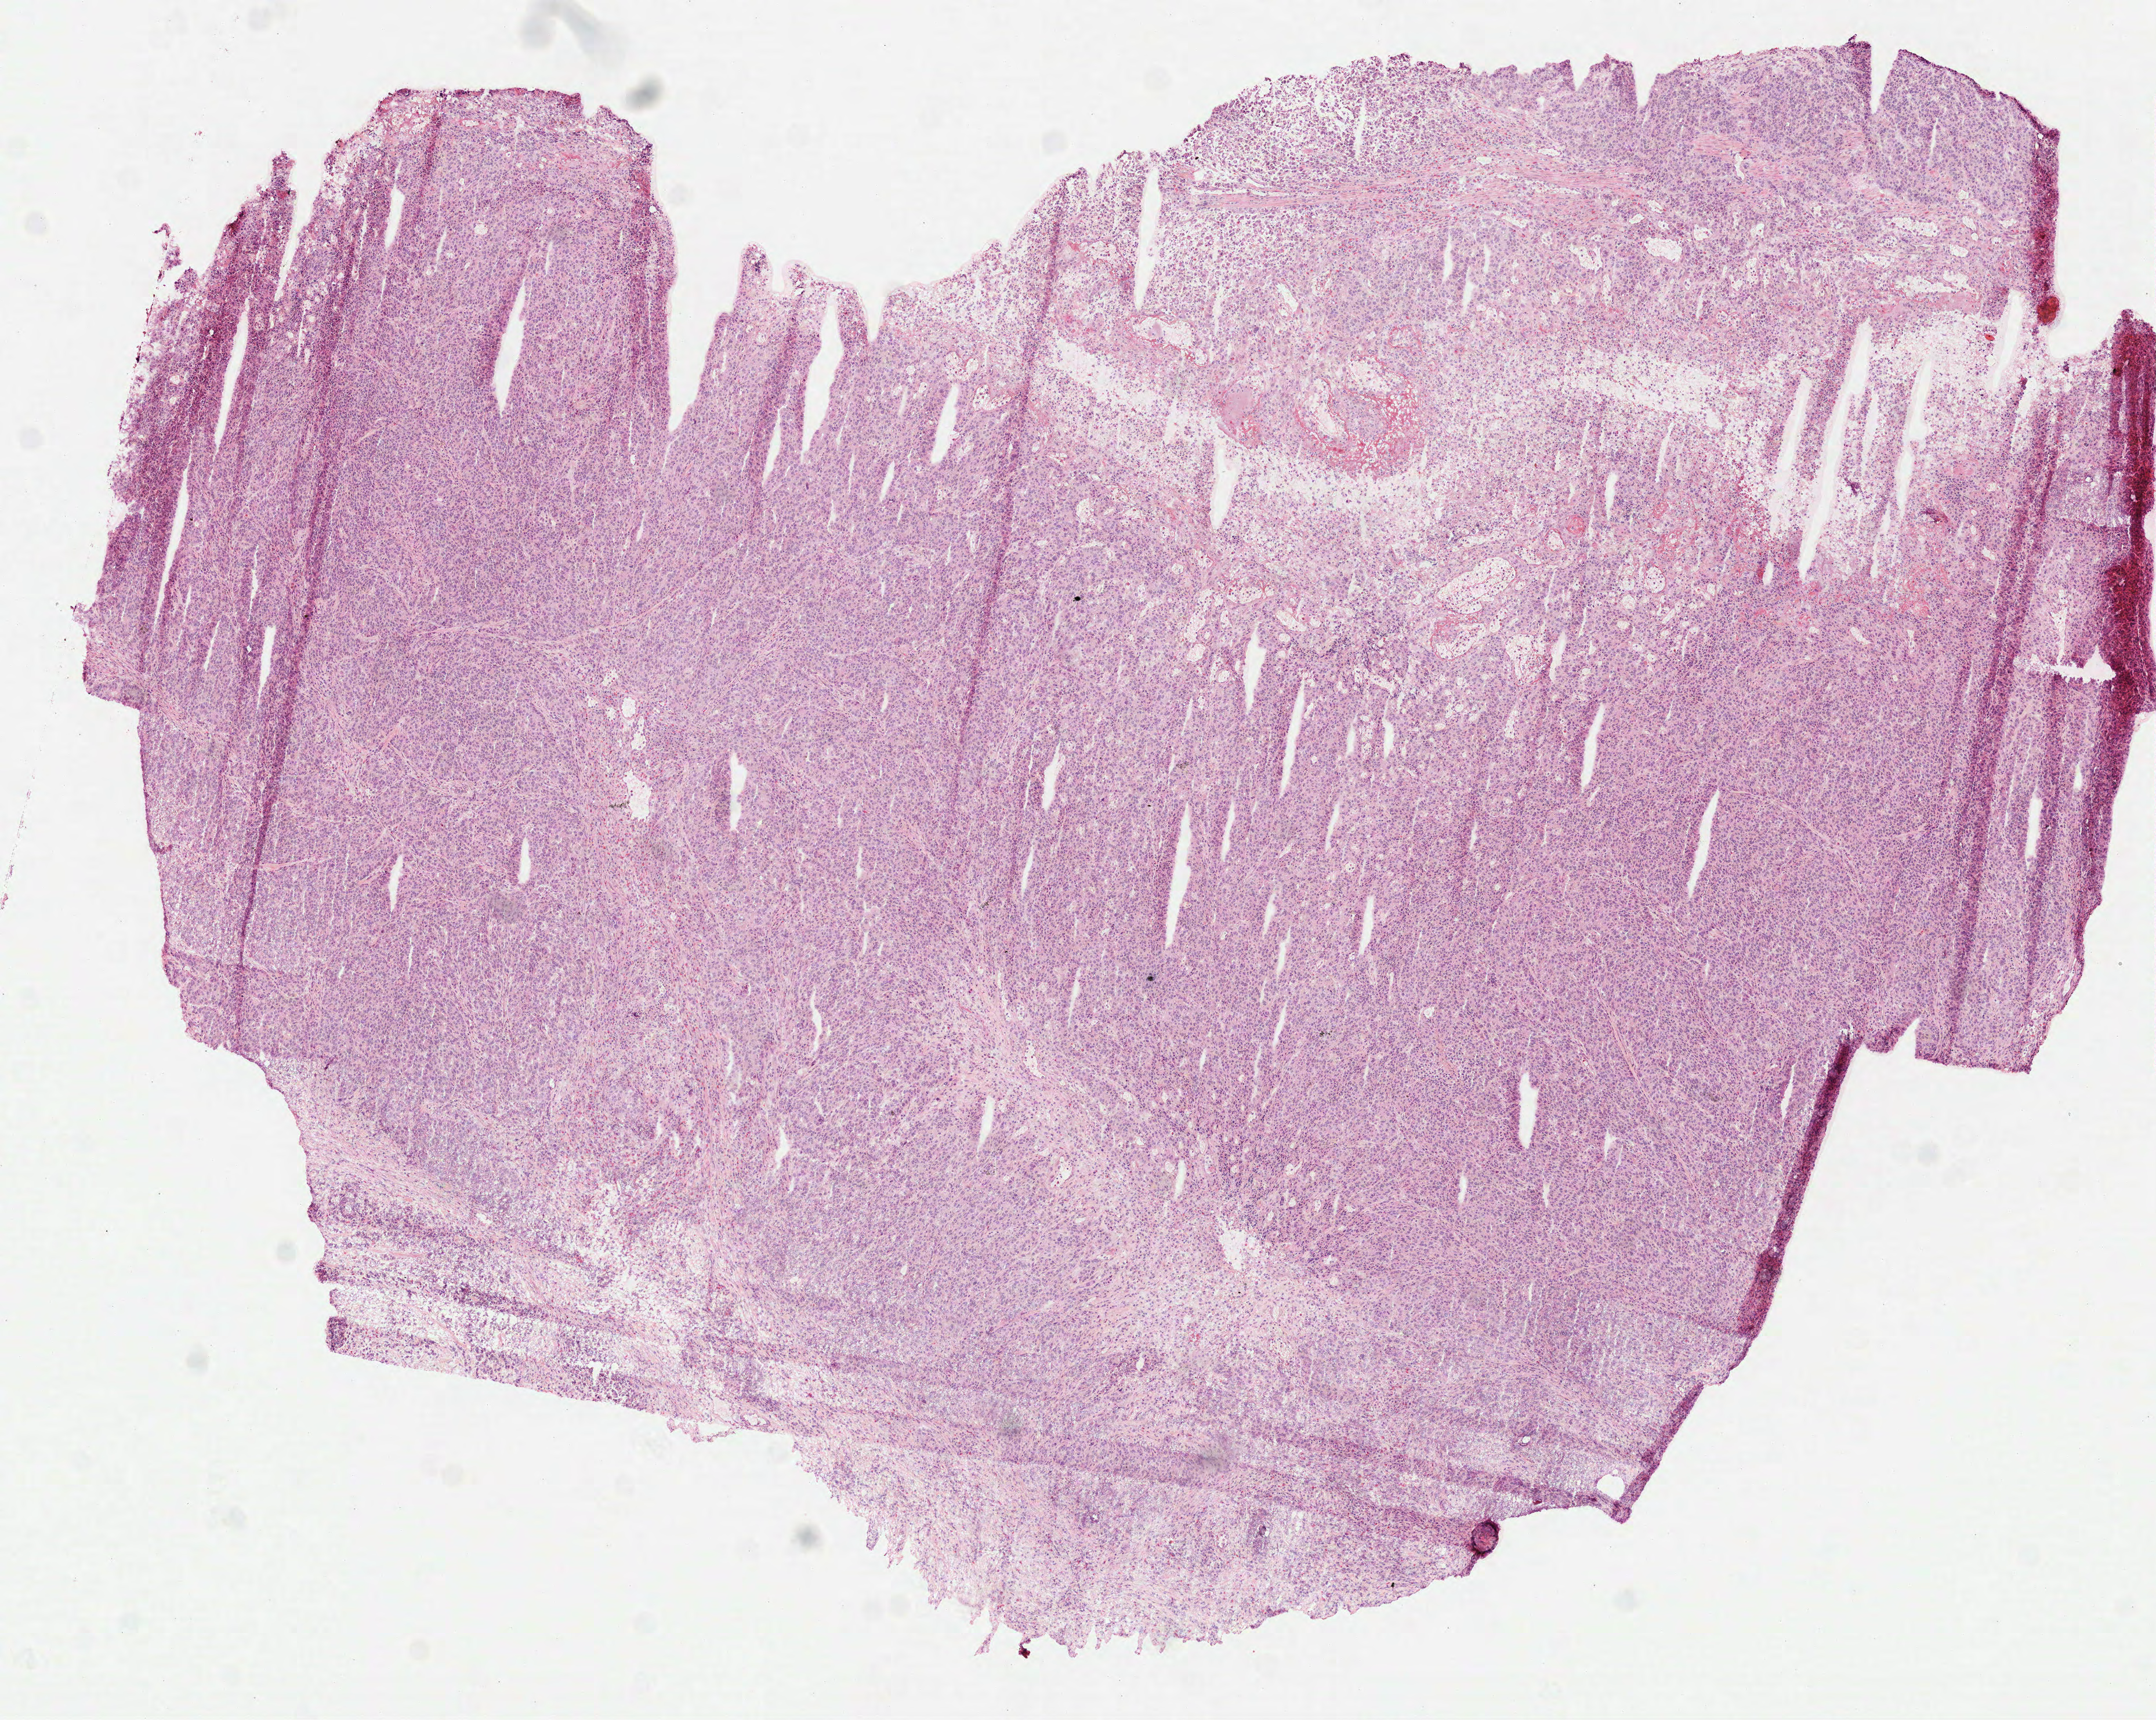
Whole-slide histology image, H&E-stained, a low-resolution overview of the entire scanned area, about 7.5 x 6.0 mm (slide scanned at 40x). Frozen section from the top of the tissue portion. Primary tumour sample from the stomach. Patient: male, age at initial diagnosis 53 years.
Pathologic diagnosis: Carcinoma, diffuse type (body of stomach).